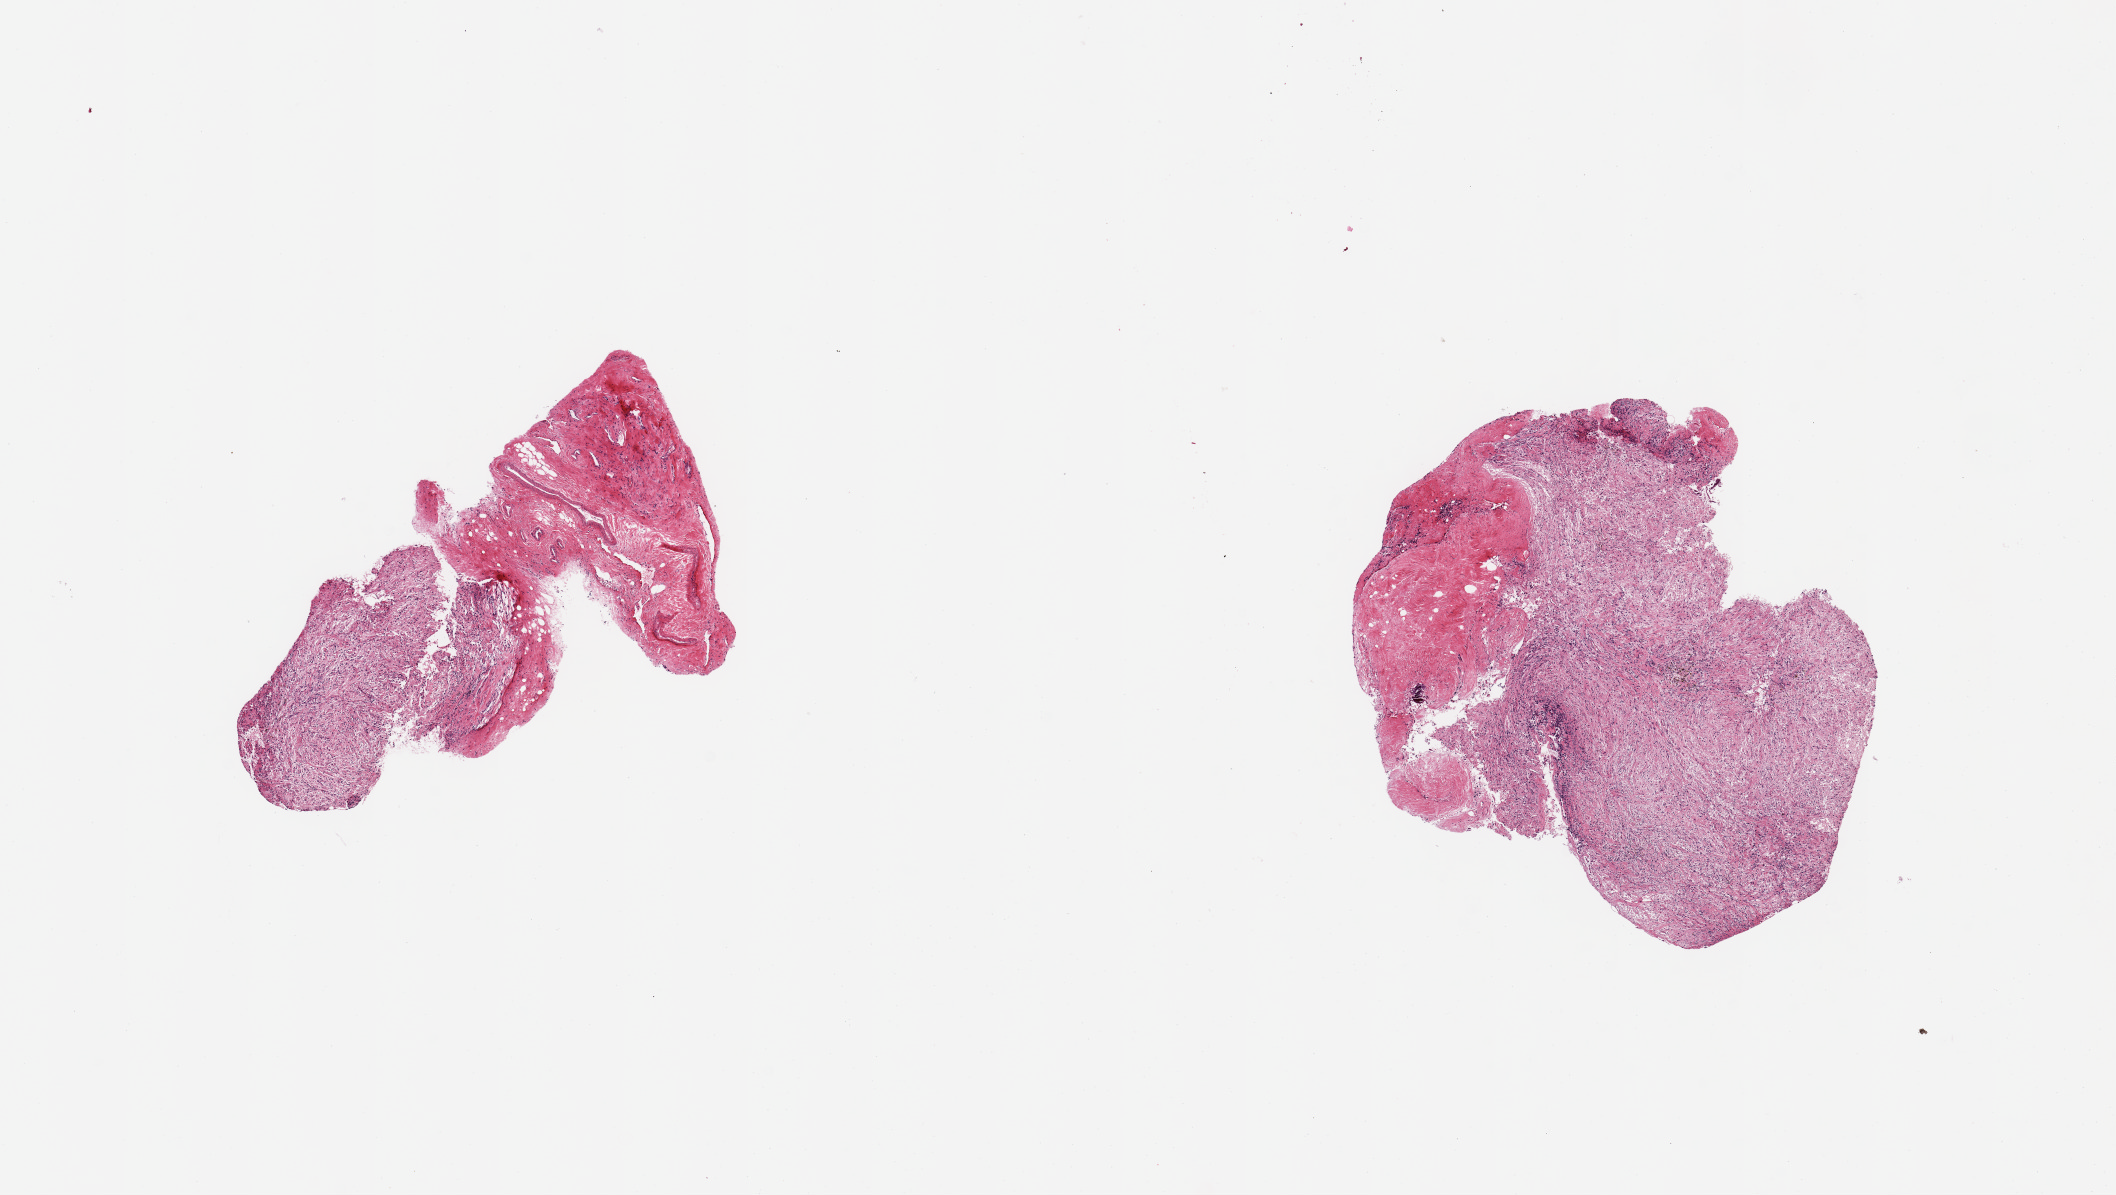
Whole-slide image, H&E stain, whole scanned area (about 16.7 x 9.5 mm, slide scanned at 20x) shown as a low-resolution overview. PAXgene-fixed, paraffin-embedded tissue. Section of pituitary (target tissue). Donor tissue sample. Male donor.
Pathologist's review note for this sample: 2 pieces; neurohypophysis with attached dense fibrous tissue.